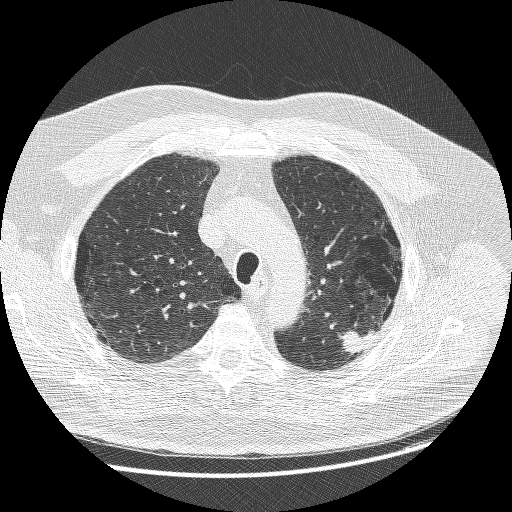
Low-dose screening chest CT, axial slice. Baseline screening round. Lung window (W 1500 / L -600 HU). 1.25 mm slice thickness. Slice 202 of 258 in the series. 512 × 512 image matrix. Male participant, aged 68 years at enrolment. Former smoker at enrolment.
• Expert reader's lesion annotation, box from (x=332, y=318) to (x=389, y=364) px.
• Reader record for this screening exam (exam-level; its link to the box is not recorded): non-calcified nodule or mass ≥4 mm, left upper lobe, 15 × 14 mm, smooth margins, soft tissue attenuation.
• Lung cancer was diagnosed 19 days after this screen: adenosquamous carcinoma, left upper lobe, poorly differentiated (G3), stage IIIB (AJCC 6th edition), 32 mm at pathology.